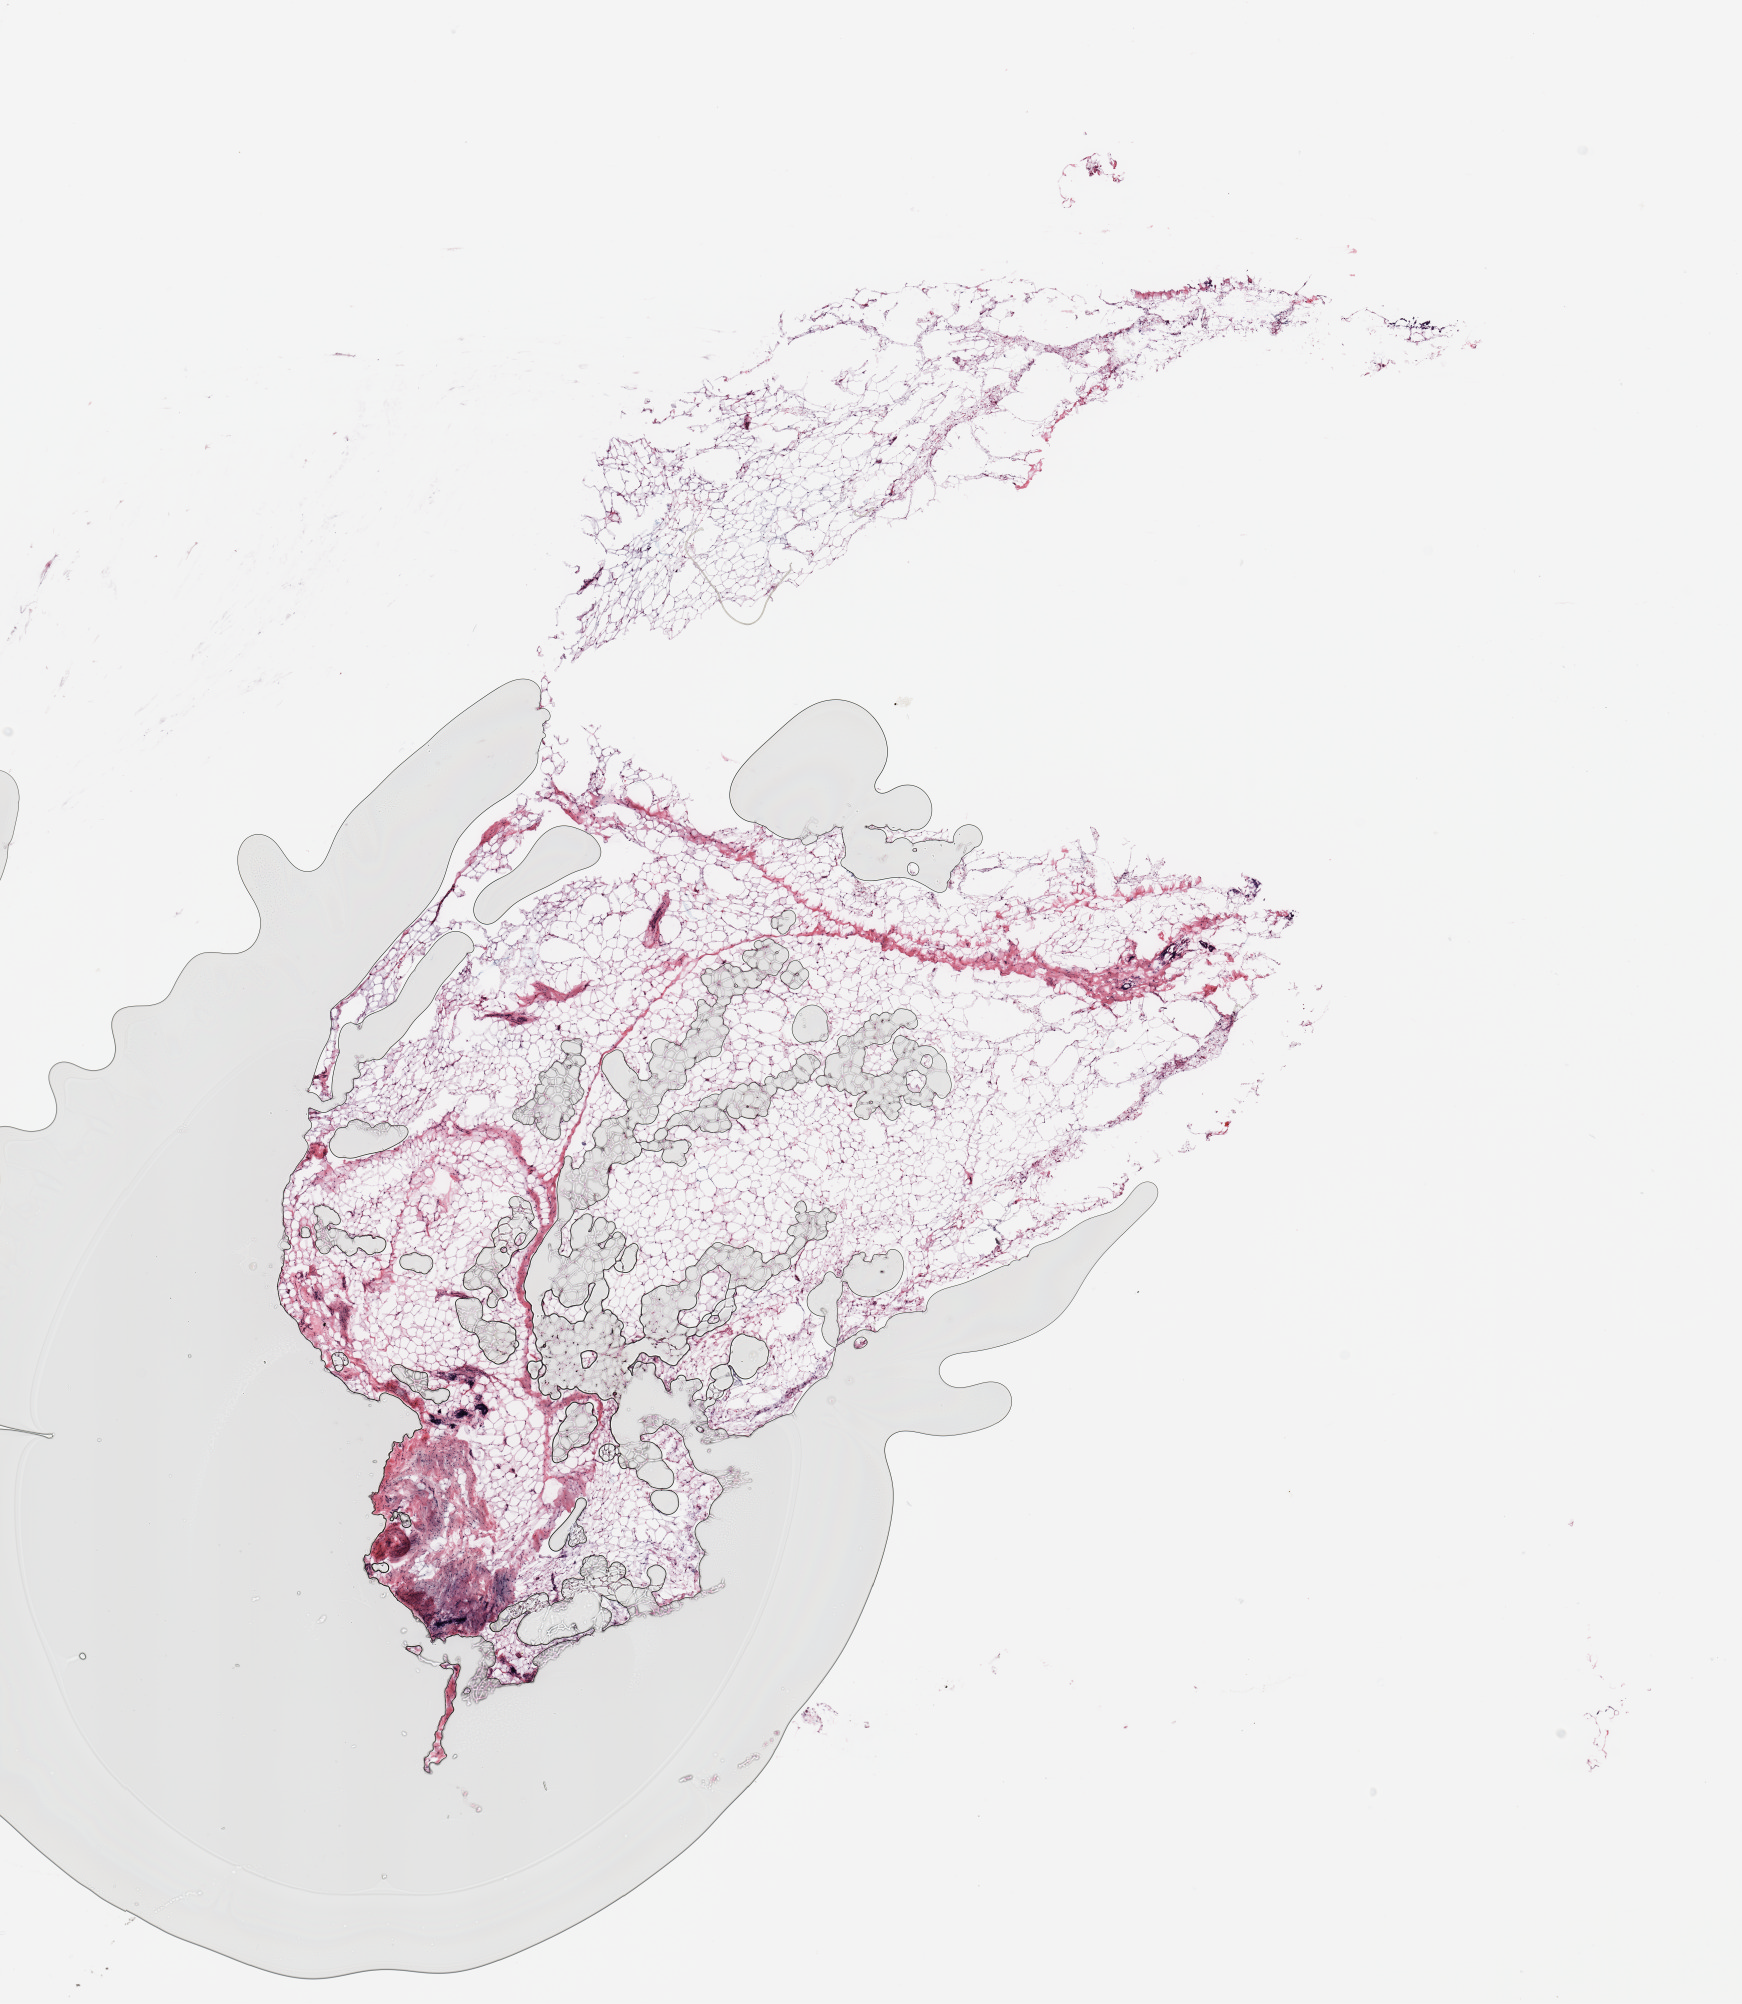
Digitized Hematoxylin and eosin (H&E) stained tissue section (whole slide) — a low-resolution overview of the entire scanned area, about 13.8 x 15.9 mm; breast, tumour tissue. 50-year-old female patient.
• diagnosis: Infiltrating duct carcinoma, NOS
• AJCC pathologic stage: IIB